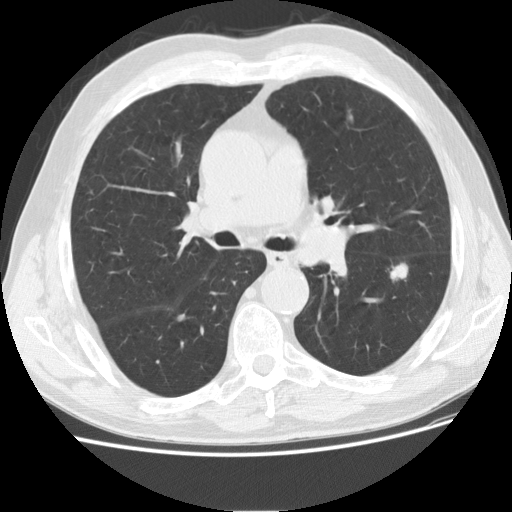
Chest CT (low-dose screening protocol), one axial image. Second annual screen. Lung window (W 1500 / L -600 HU). 2.5 mm slice thickness. Standard (soft-tissue) reconstruction kernel (STANDARD). Slice 66 of 175 in the series. Male participant, aged 73 years at enrolment. Current smoker at enrolment.
Expert reader's lesion annotation, bounding box <366,253,425,302> (left, top, right, bottom; pixels). Reader record for this screening exam (exam-level; its link to the box is not recorded): non-calcified nodule or mass ≥4 mm, left lower lobe, 16 × 10 mm, smooth margins, soft tissue attenuation, pre-existing on the prior screen: yes; interval growth: yes. Lung cancer was diagnosed 76 days after this screen: adenocarcinoma, NOS, left lower lobe, poorly differentiated (G3), stage IIA (AJCC 6th edition), 12 mm at pathology.